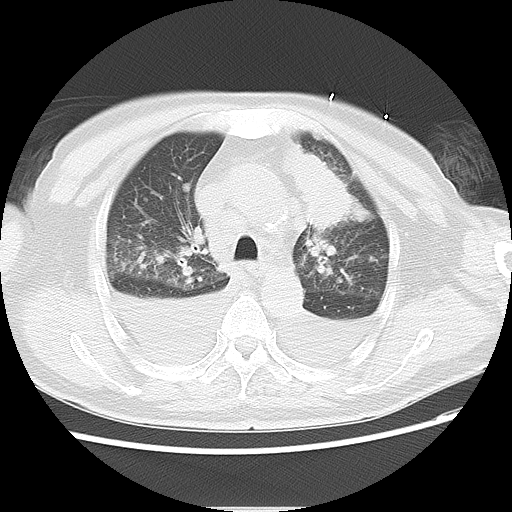
Chest CT, one axial slice; position 18 of 22 along the scan axis; 120 kVp; lung window (W 1500 / L -600 HU); 5 mm slice thickness; 512 × 512 image matrix. Patient: male, 66 years. From the clinical record (not read from this slice): clinical TNM (as recorded): T1c N0 M0.
Structures marked on this image (rectangle marked by the reading radiologist):
- lung tumour (recorded histology: adenocarcinoma): bounding box [x1, y1, x2, y2] px = [275, 139, 370, 230]